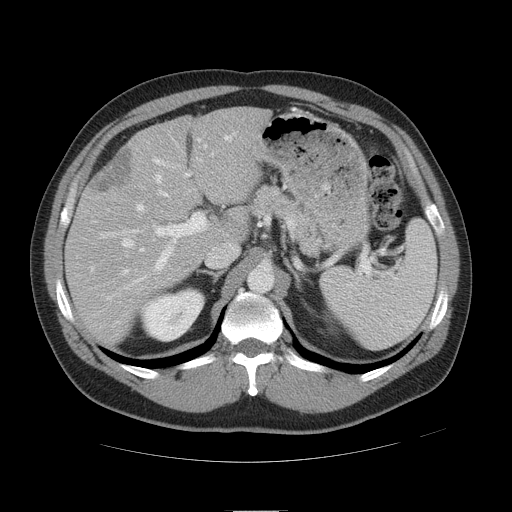
Contrast-enhanced abdominal CT, one axial slice; slice 30 of 49 in the series (ordered by position); intravenous contrast given; soft-tissue window (W 400 / L 40 HU); 5 mm slice thickness; 512 × 512 image matrix. Male patient, age 52 years. Case-level facts recorded for this patient, not image findings: diagnosis: colorectal cancer liver metastases, imaged before liver resection; multiple liver metastases: yes; largest metastasis: 5.1 cm; disease in both lobes: yes.
Structures marked on this image (manually delineated by an expert):
- hepatic veins: bounding box [x1, y1, x2, y2] px = [122, 138, 207, 274]
- liver: [67, 108, 266, 344]
- planned liver remnant (the part of the liver to remain after resection): [133, 108, 266, 238]
- portal vein (with intrahepatic branches): [100, 136, 230, 300]
- liver metastasis: [91, 150, 135, 195]